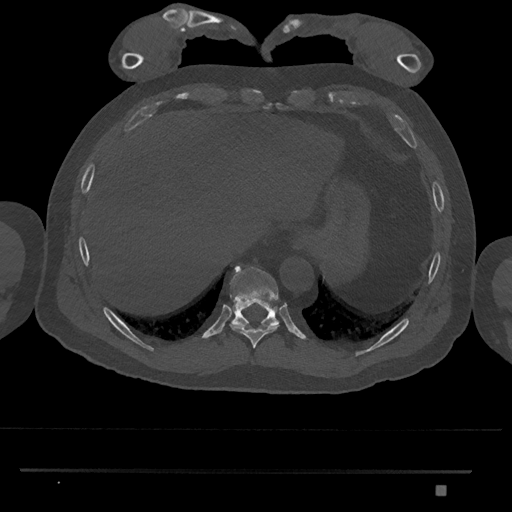
CT including the spine, one axial slice; slice 1031 of 1134 in the series (ordered by position); reconstruction kernel Br40s/3; 120 kVp; bone window (W 1800 / L 400 HU); 0.5 mm slice thickness; 512 × 512 image matrix, field of view 429 × 429 mm. Patient: male, 65 years. Case-level facts recorded for this patient, not image findings: primary cancer: prostate.
Outlined on this slice (semi-automatically segmented with operator editing):
- T10 vertebra: box from (x=224, y=265) to (x=279, y=335) px
- T9 vertebra: (x=230, y=322)–(x=279, y=349)